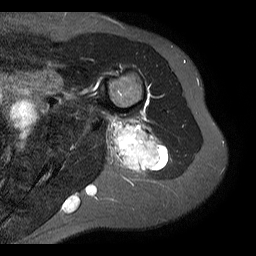
MRI of an extremity soft-tissue mass, one axial slice; slice 9 of 20 in the series (ordered by position); STIR; 256 × 256 image matrix. Female patient. From the clinical record (not read from this slice): histological type: malignant fibrous histiocytoma; grade: low; site of the primary tumour: left arm.
Structures marked on this image (expert manual segmentation):
- gross tumour volume (mass): bounding box <105,118,170,173> (left, top, right, bottom; pixels)